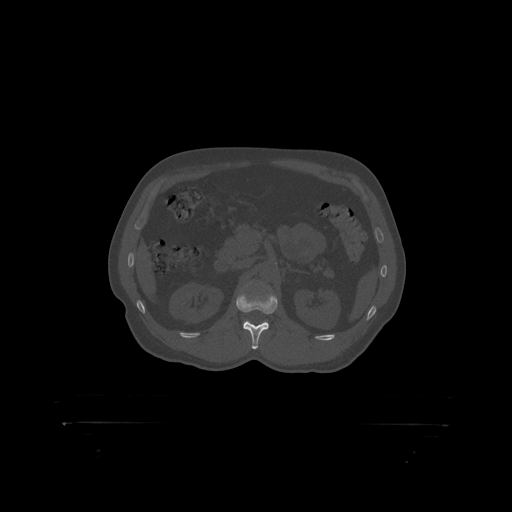
CT including the spine, one axial slice; position 317 of 399 along the scan axis; reconstruction kernel STANDARD; bone window (W 1800 / L 400 HU); 1.25 mm slice thickness; 512 × 512 image matrix, field of view 650 × 650 mm. Patient: male, 46 years. Case-level facts recorded for this patient, not image findings: primary cancer: skin.
Annotated regions visible in this slice (semi-automatically segmented with operator editing):
- L1 vertebra: box from (x=237, y=295) to (x=278, y=314) px